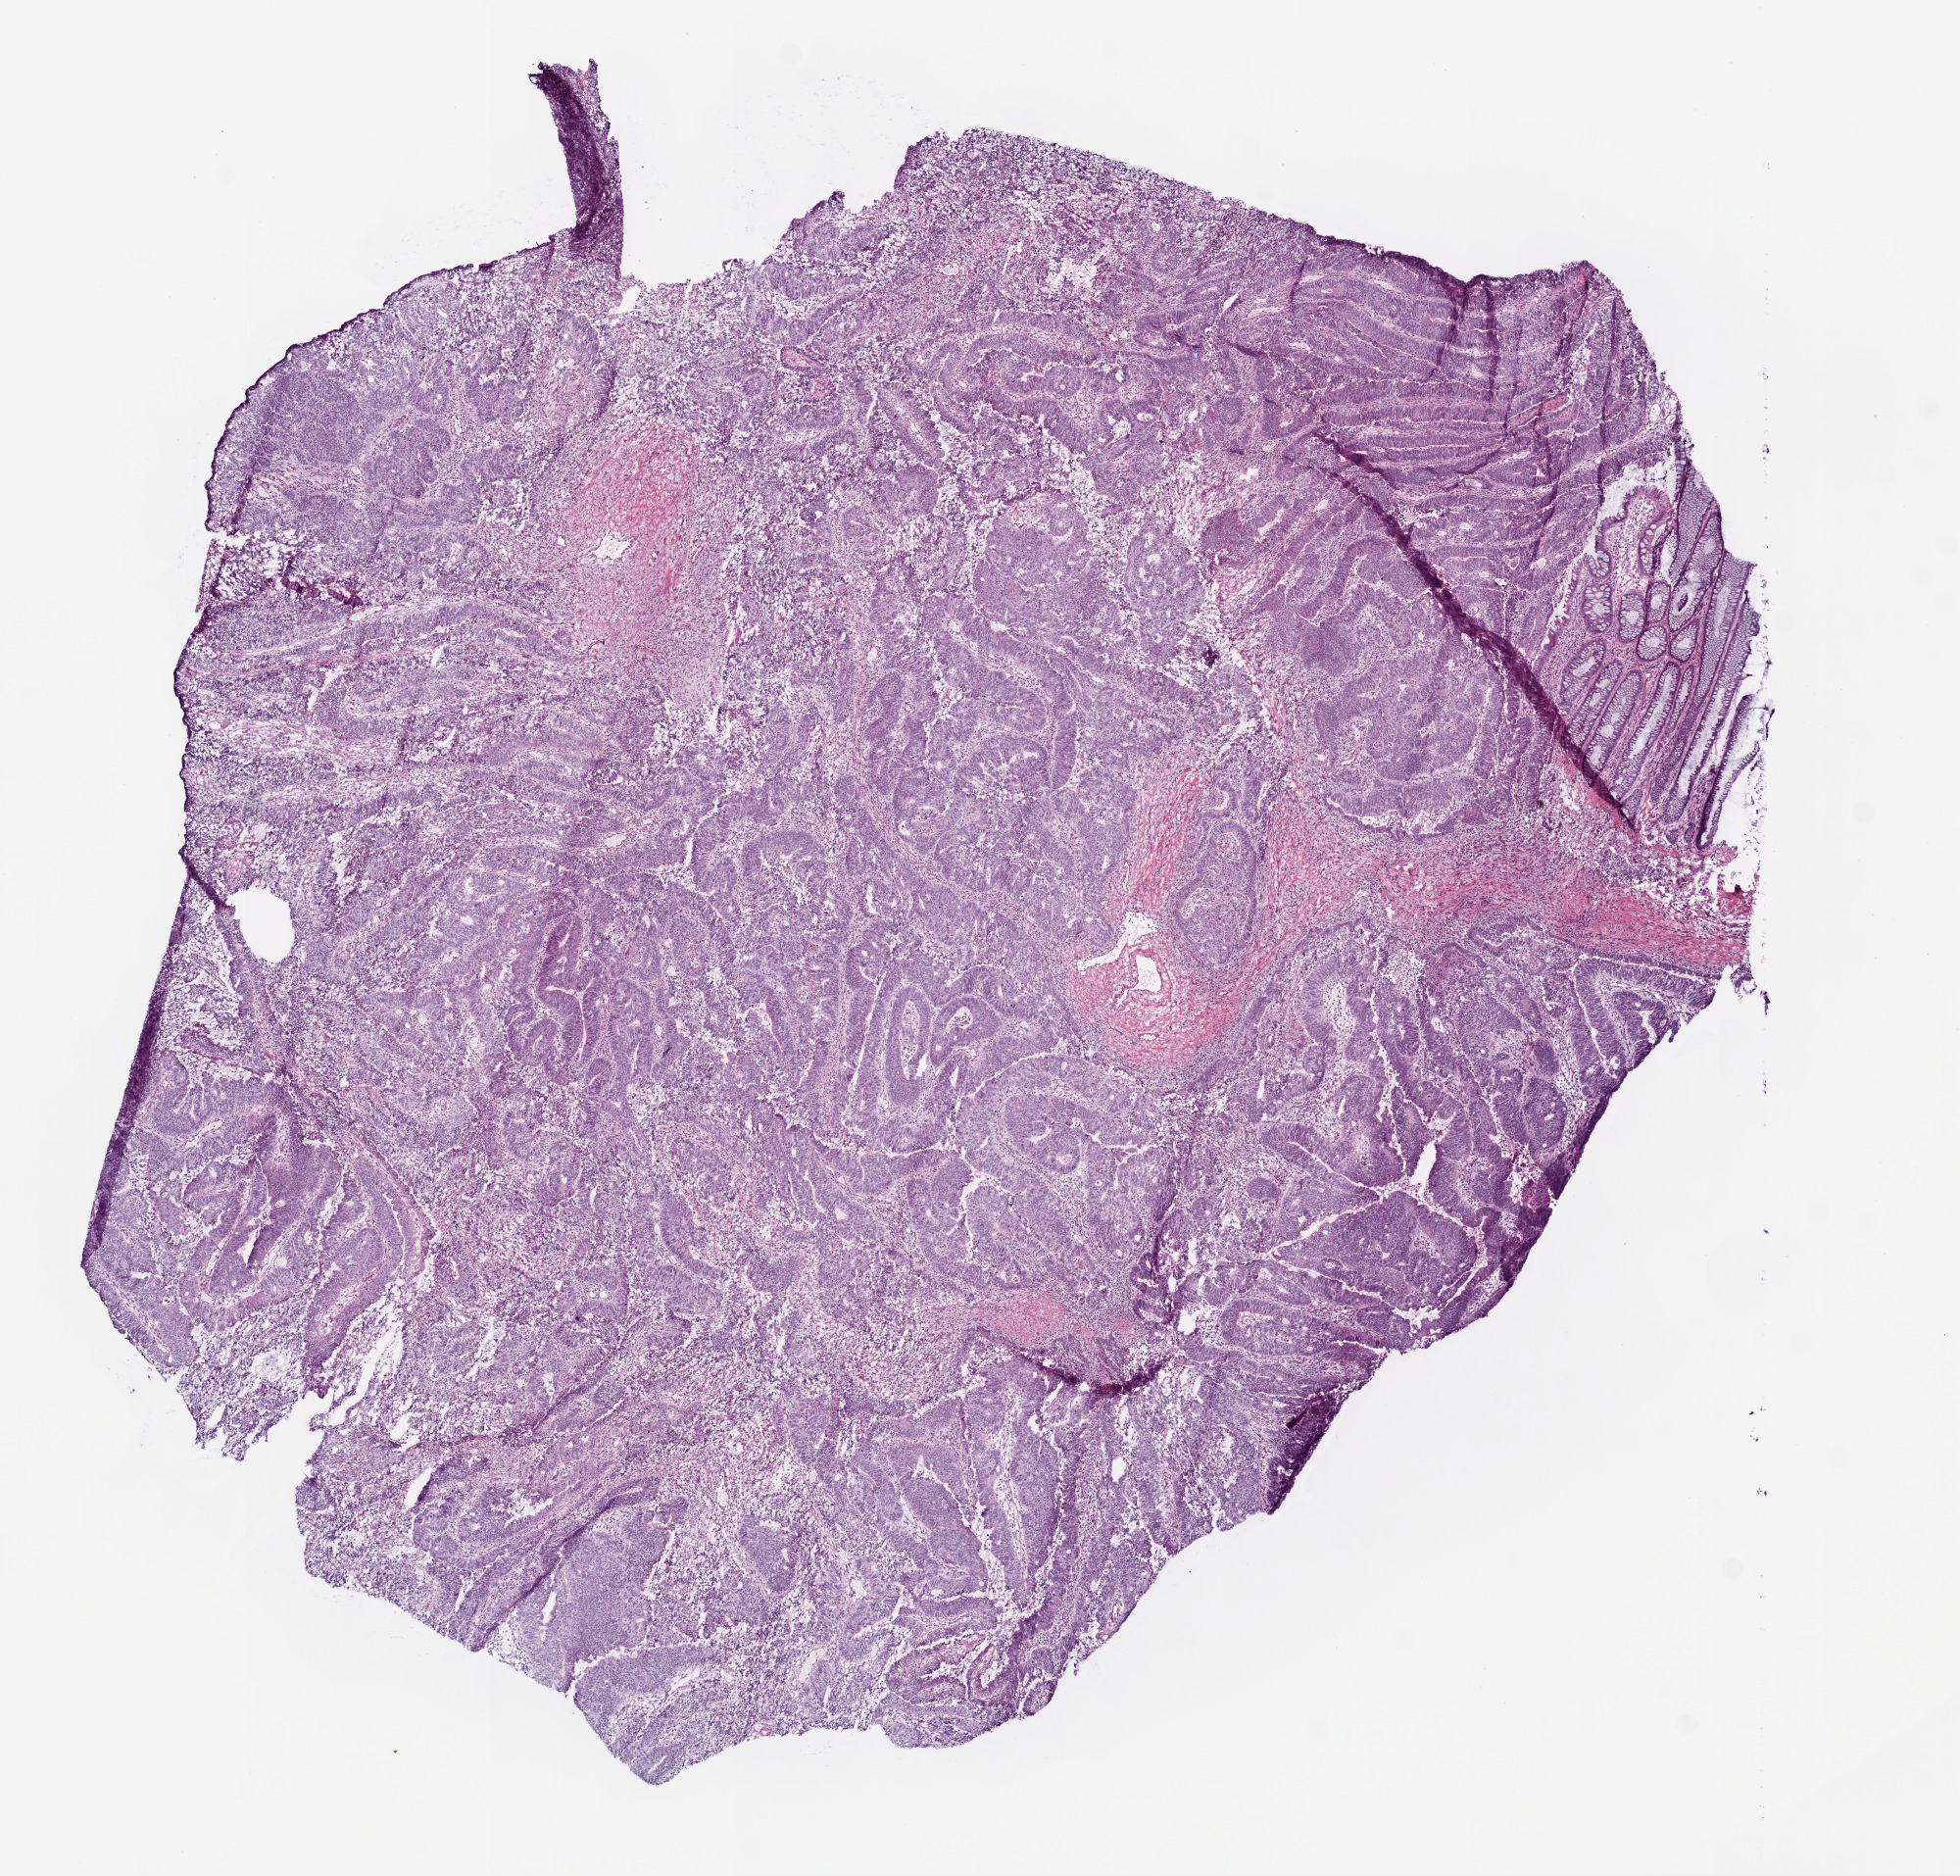
Whole-slide histology image, H&E-stained, whole scanned area (about 8.0 x 7.7 mm) shown as a low-resolution overview; frozen section from the bottom of the tissue portion; sample: primary tumour, colon. Female patient. Slide review estimates, as recorded: tumour cells 90%, tumour nuclei 85%, normal cells 2%, stromal cells 7%, necrosis 1%. Infiltration values recorded for this section: lymphocyte infiltration 10%, neutrophil infiltration 1%.
- lymph nodes positive (case pathology): 0 of 19 examined
- pathologic diagnosis: Adenocarcinoma, NOS
- AJCC pathologic stage: I